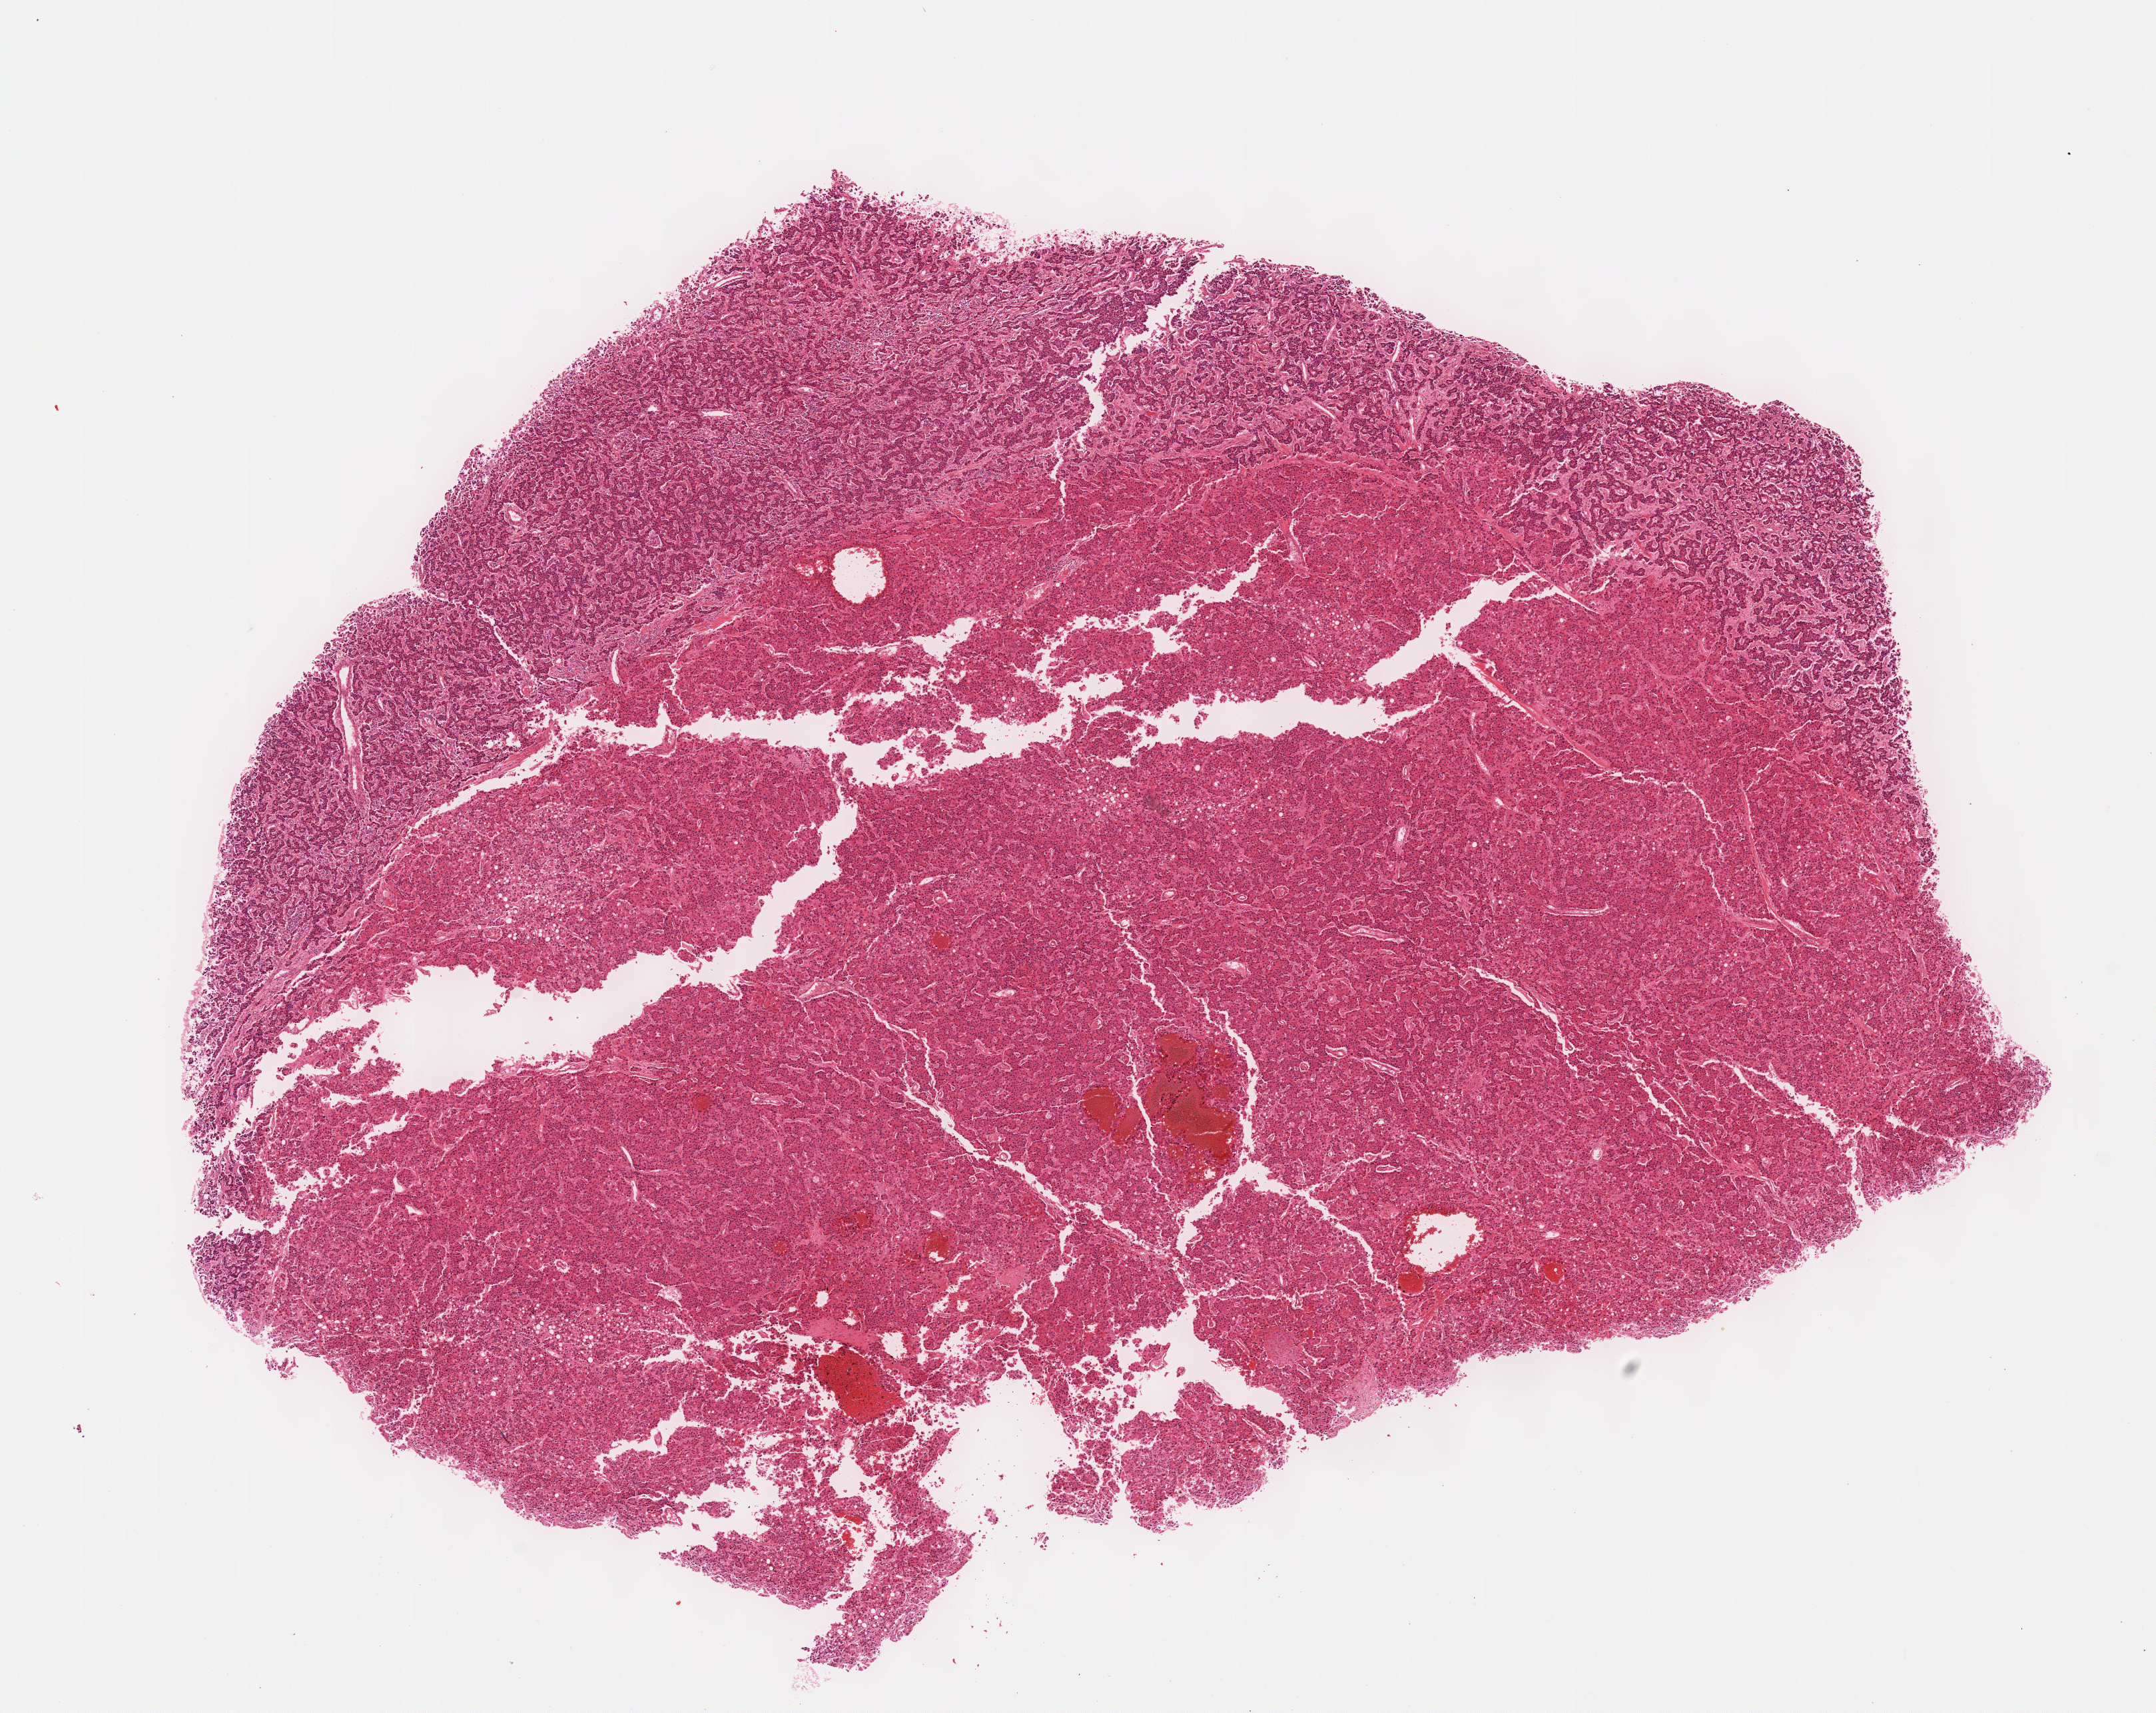
H&E whole-slide image — shown as a low-resolution overview of the whole scanned area (about 13.1 x 10.4 mm, acquisition: 40x scan), formalin-fixed paraffin-embedded (FFPE) diagnostic section, sample: primary tumour, liver. Patient: female, age at initial diagnosis 73 years. Histologic grade: G2 (moderately differentiated).
AJCC pathologic stage: I. Diagnosis: Hepatocellular carcinoma, NOS. TNM: T1 N0 M0.